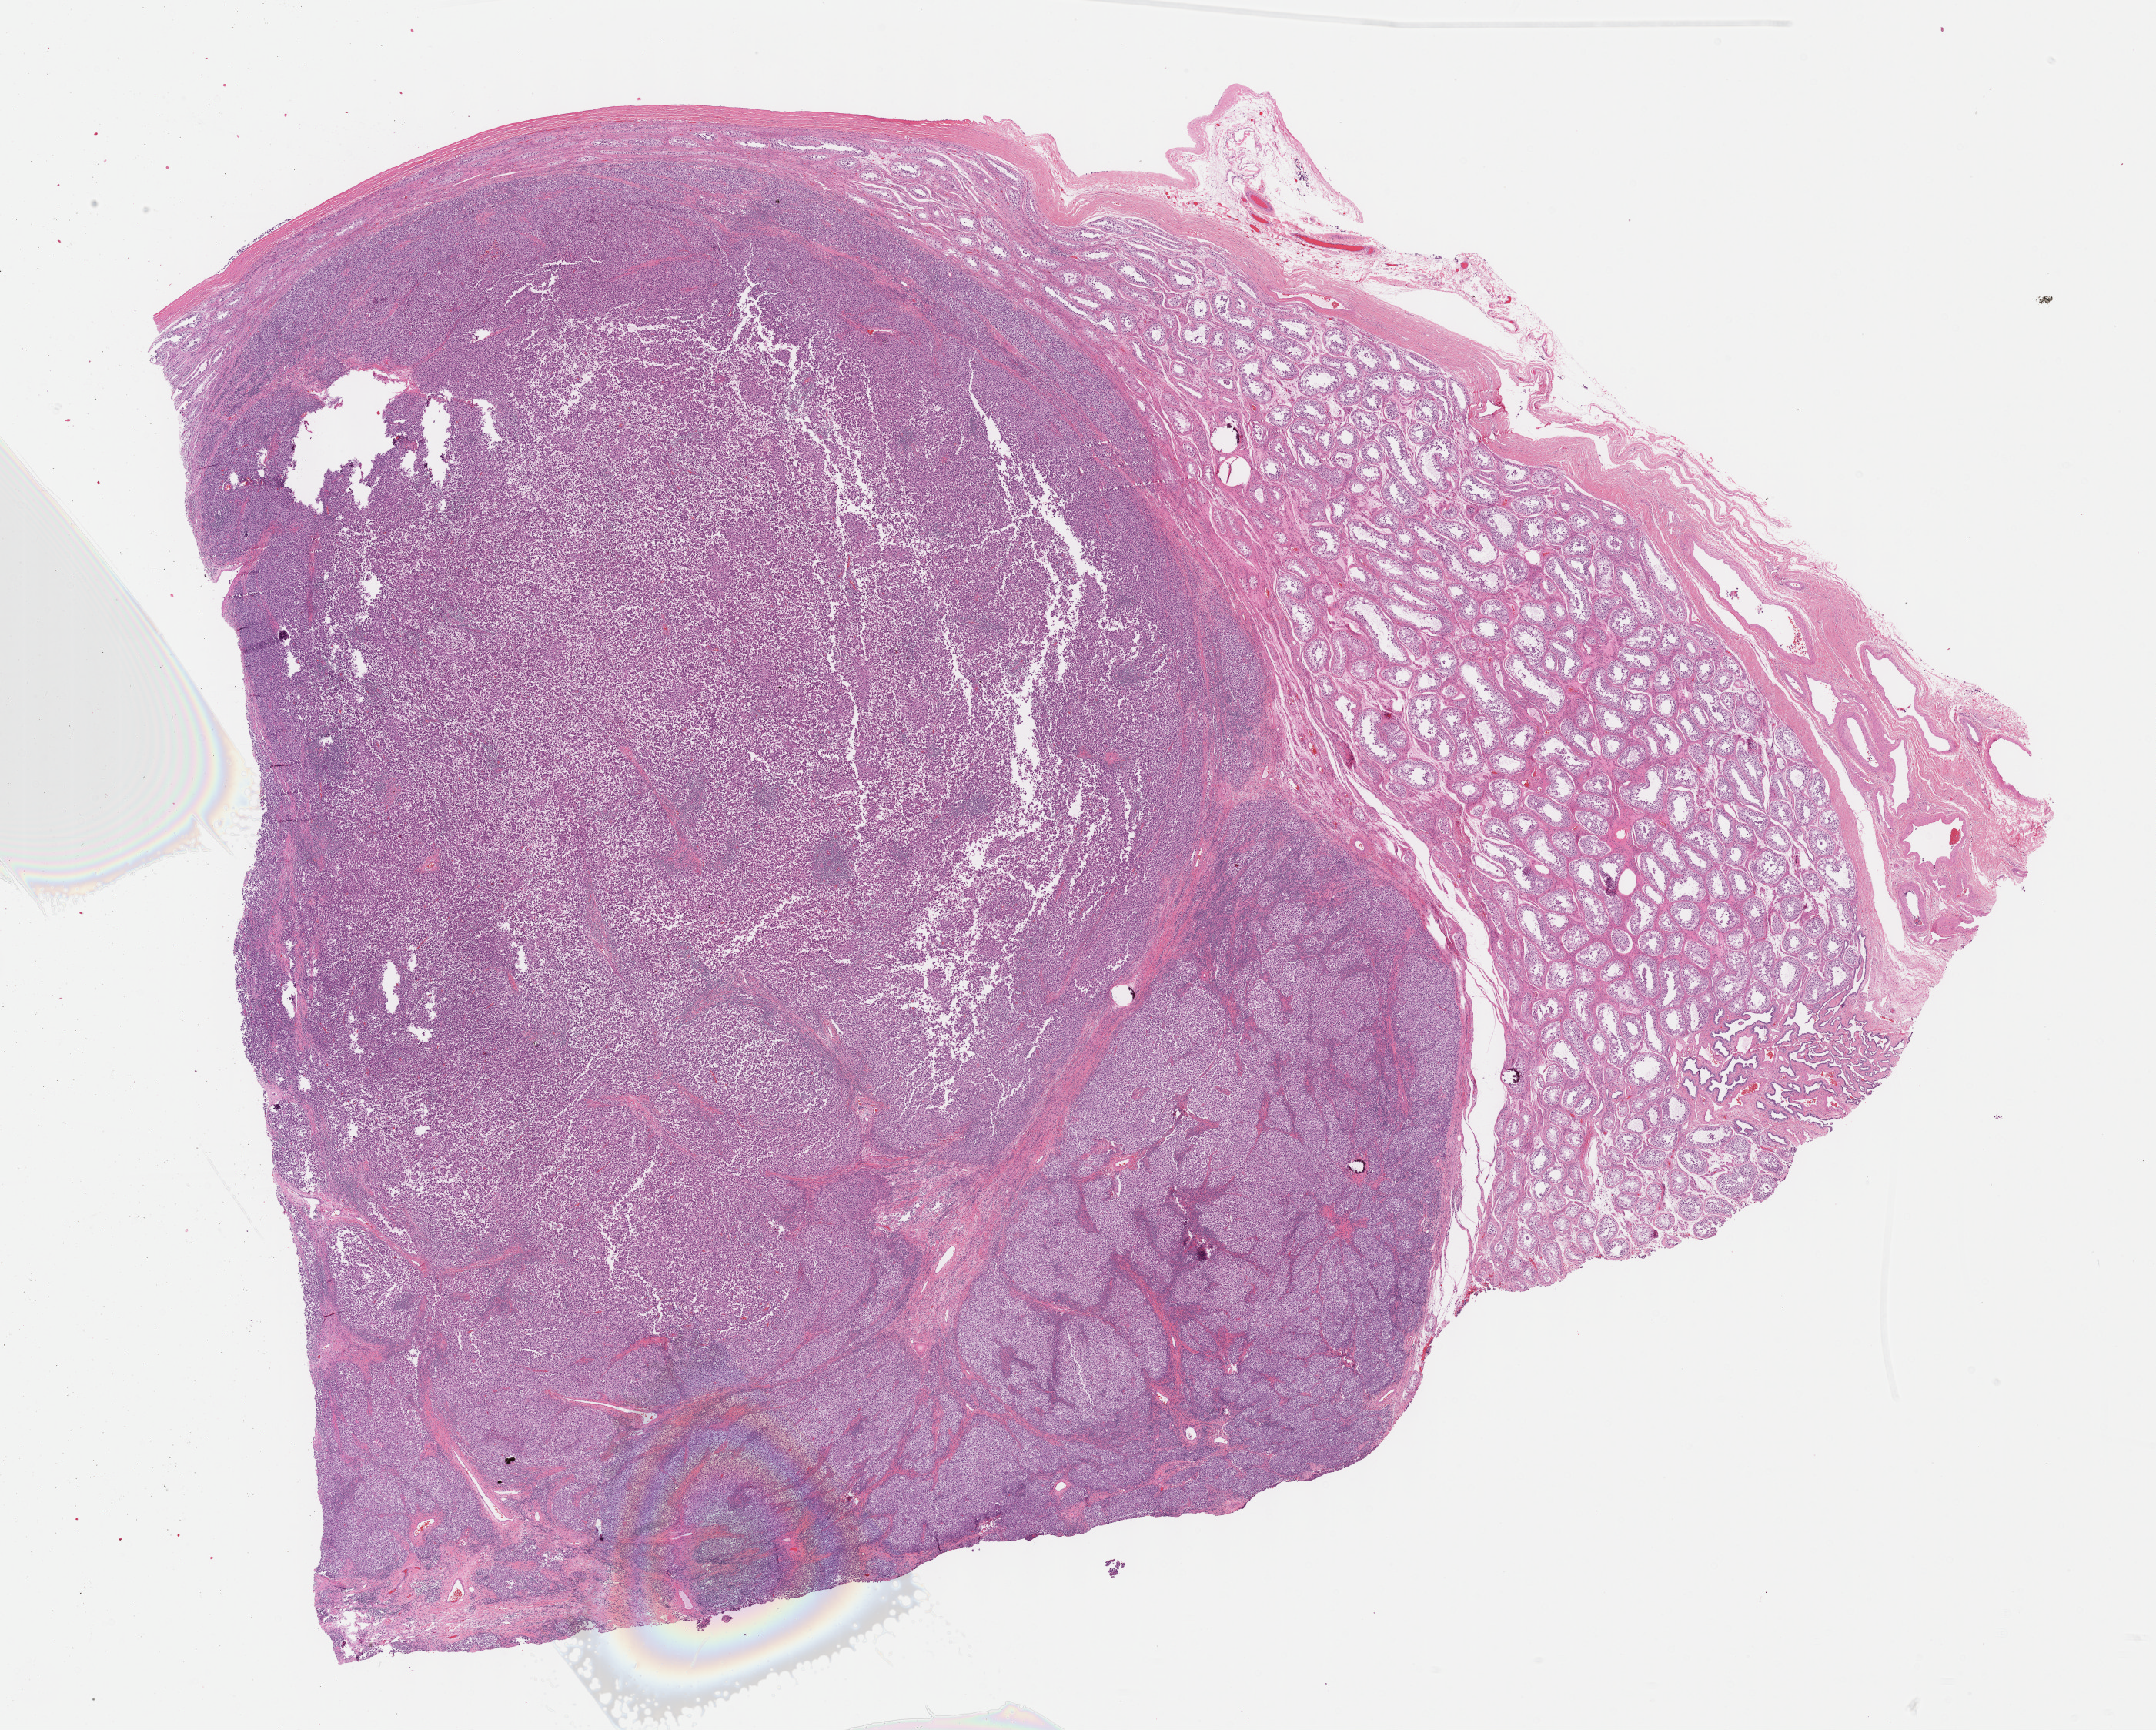
Digitized H&E tissue section (whole slide), a low-resolution overview of the entire scanned area, about 22.7 x 18.2 mm (acquisition: 40x scan); formalin-fixed paraffin-embedded (FFPE) diagnostic section; testis, primary tumour sample. Male patient; age at initial diagnosis 38 years.
Pathologic diagnosis: Seminoma, NOS. Laterality: left.